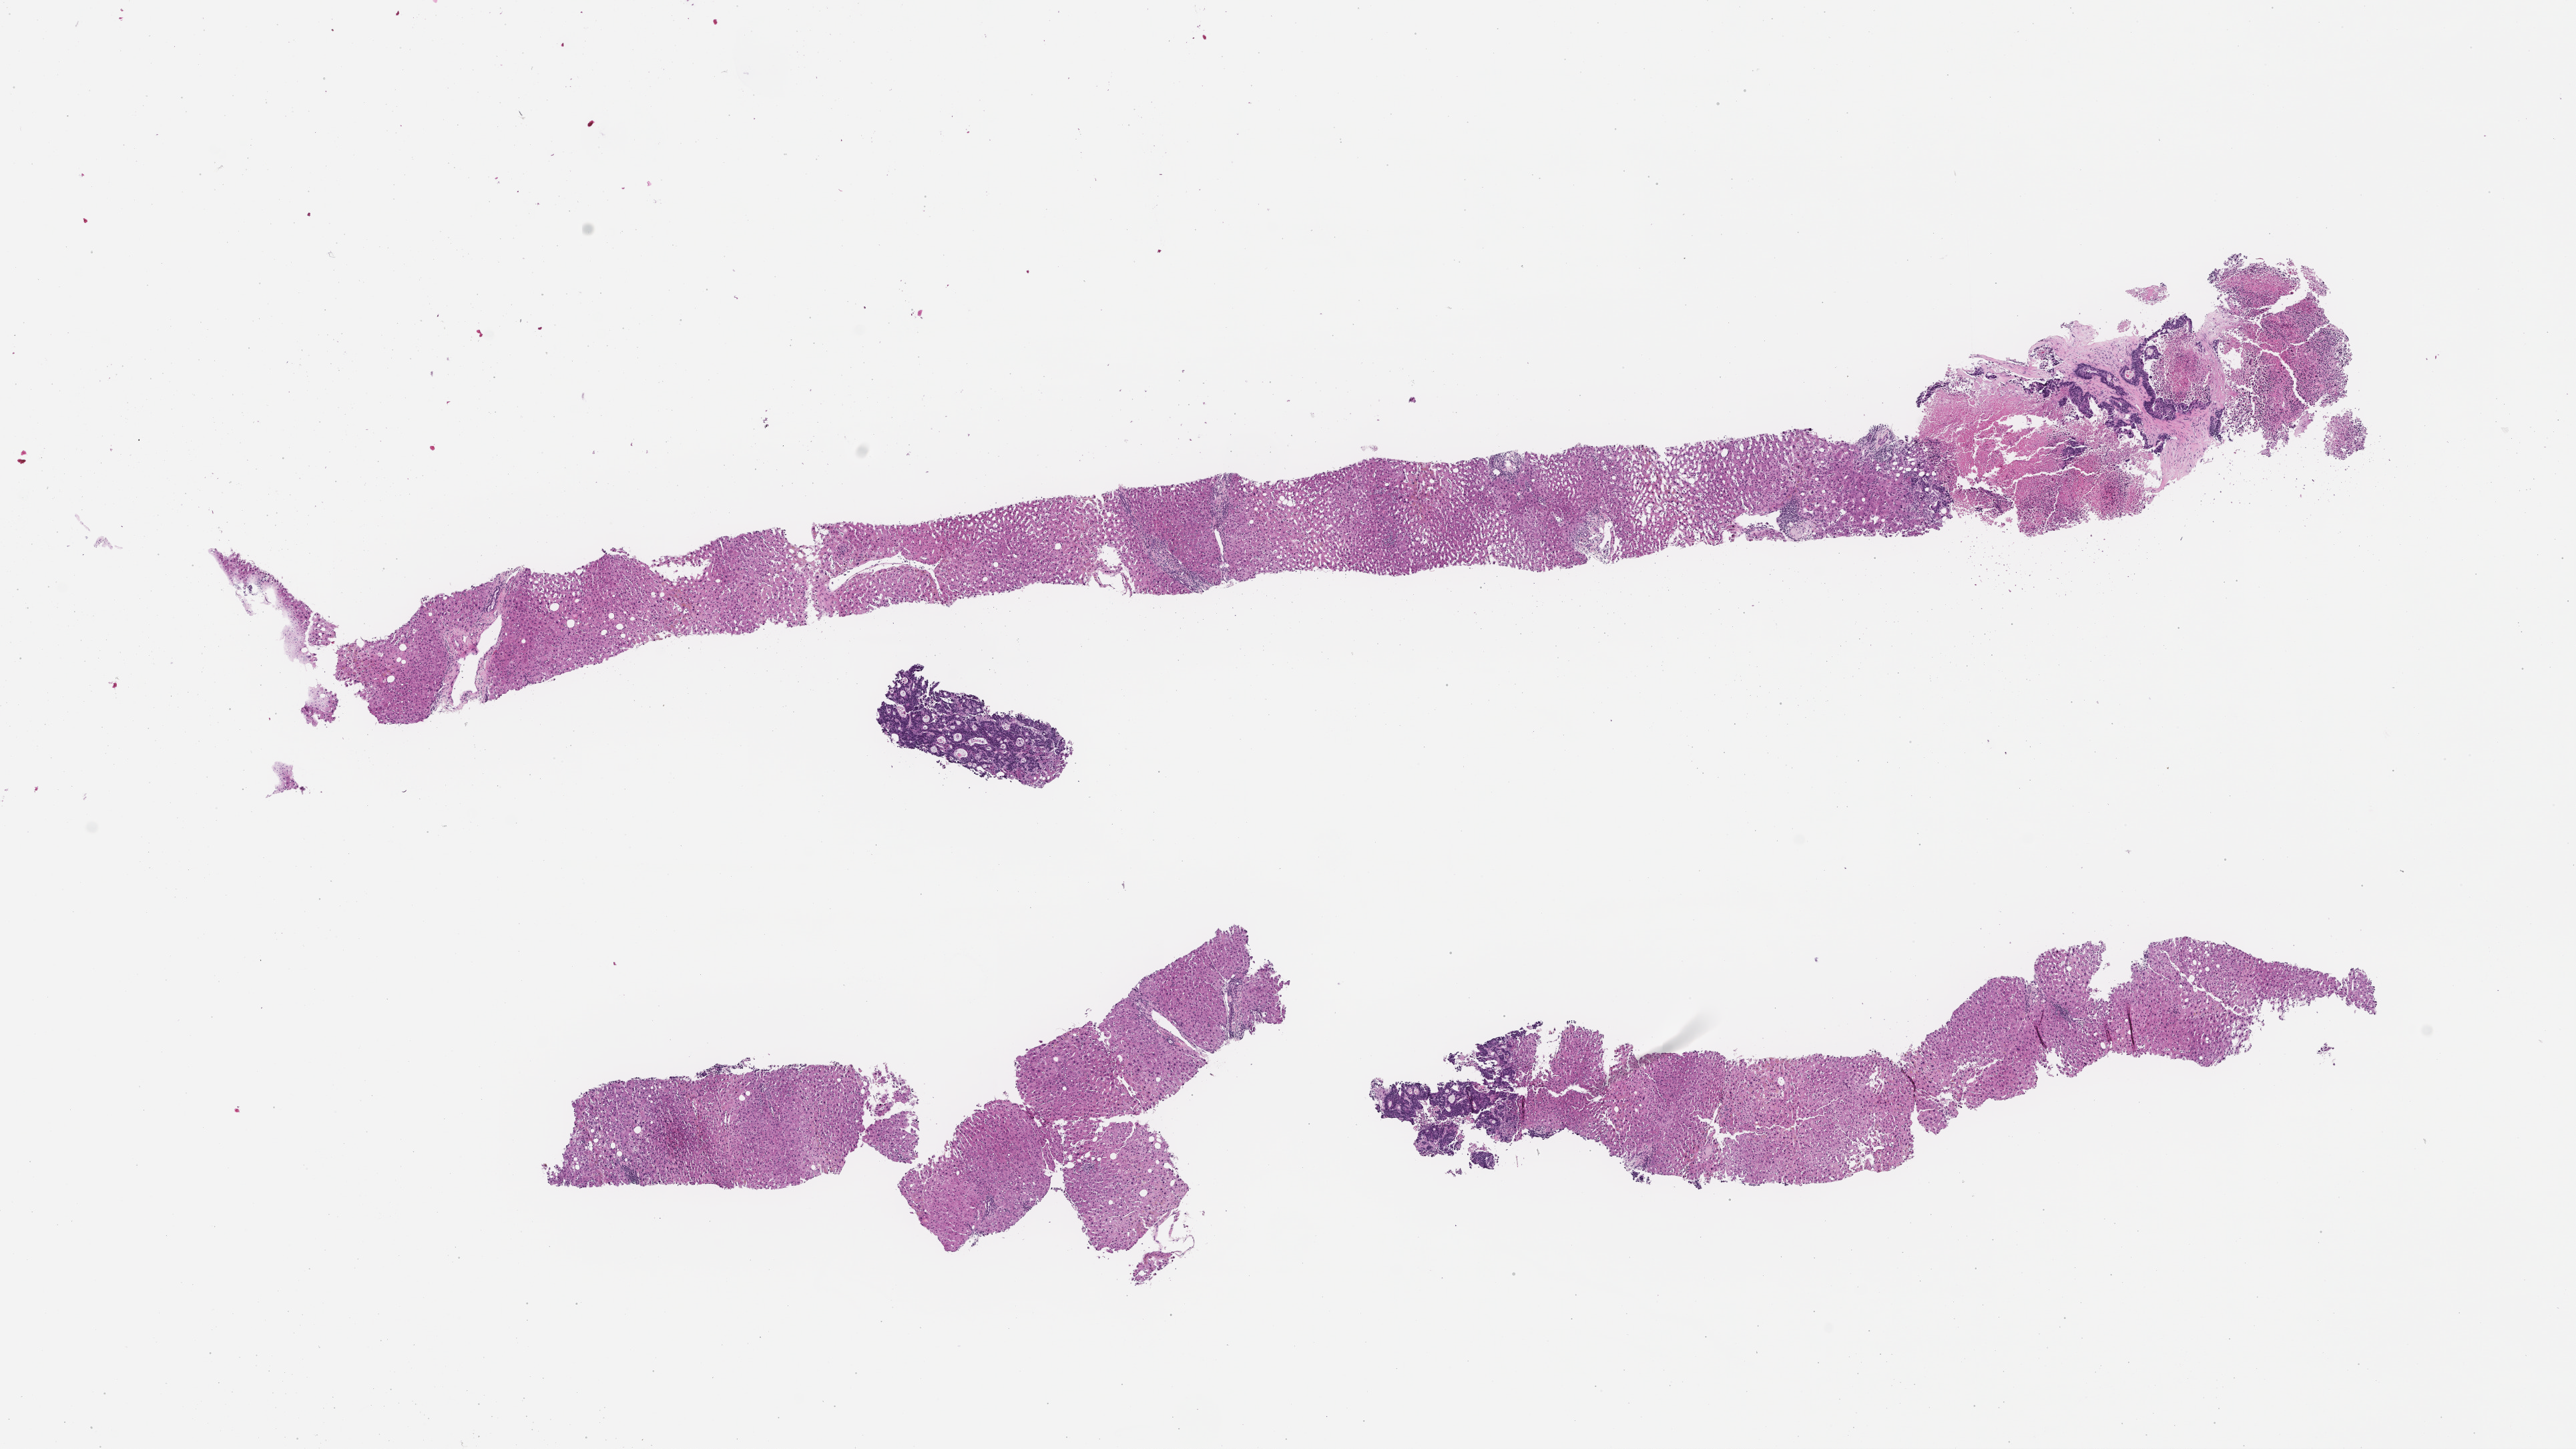
Digitized haematoxylin and eosin-stained section, low-resolution overview of the scanned area, about 15.6 x 8.8 mm; FFPE section. Patient: male.
- this section: metastatic tumor tissue
- primary diagnosis of the patient: Colorectal Carcinoma